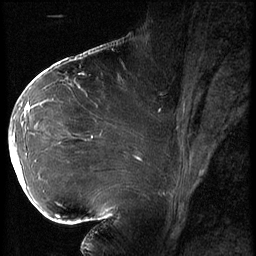
Breast MRI (dynamic contrast-enhanced), one sagittal slice. Position 36 of 62 along the scan axis. 3 images stored at this slice position (order not interpretable as contrast timing). 1.5 T. TE 4.2 ms, TR 9 ms. 2.5 mm slice thickness. 256 × 256 image matrix. Female patient, age 43 years. From the clinical record (not read from this slice): setting: breast cancer imaged before/during neoadjuvant chemotherapy; receptor status: HER2-positive.
Outlined on this slice (semi-automatically segmented with operator editing):
- analysis volume of interest (the breast-tissue region the enhancement analysis was run in; not a lesion): bounding box <10,90,82,203> (left, top, right, bottom; pixels)
- tumour enhancement mask (voxels above the 140 % enhancement threshold inside the analysis volume of interest): <11,103,41,187>